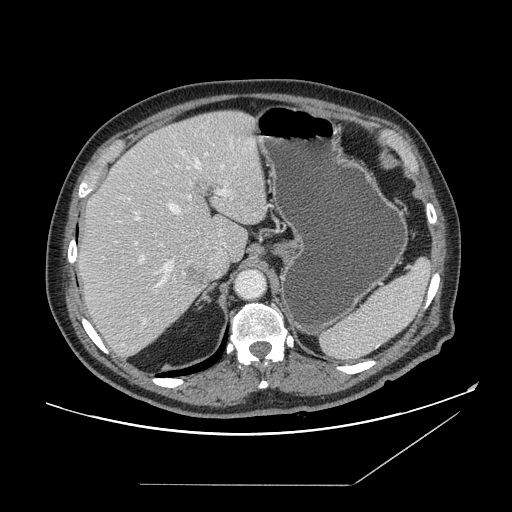
Contrast-enhanced abdominal CT, one axial slice; position 112 of 166 along the scan axis; soft-tissue window (W 400 / L 40 HU); 2.5 mm slice thickness; 512 × 512 image matrix, field of view 416 × 416 mm. Male patient, age 80 years. Case-level facts recorded for this patient, not image findings: diagnosis: colorectal cancer liver metastases, imaged before liver resection; multiple liver metastases: no; largest metastasis: 2.2 cm; disease in both lobes: no.
Outlined on this slice (manually delineated by an expert):
- hepatic veins: bounding box (x1, y1, x2, y2) in pixels: (136, 157, 223, 289)
- liver: (78, 111, 268, 357)
- planned liver remnant (the part of the liver to remain after resection): (84, 111, 267, 261)
- portal vein (with intrahepatic branches): (129, 153, 229, 323)
- liver metastasis: (189, 268, 204, 286)
- liver metastasis: (185, 267, 205, 284)